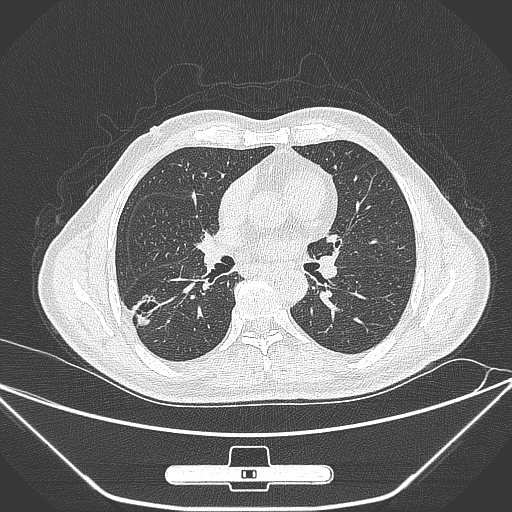
Chest CT, one axial slice; 120 kVp; lung window (W 1500 / L -600 HU); 512 × 512 image matrix, field of view 398 × 398 mm. Patient: male, 71 years. From the clinical record (not read from this slice): clinical TNM (as recorded): T1c N0 M0; histopathological grade: G2.
Outlined on this slice (bounding box drawn by a radiologist):
- lung tumour (recorded histology: adenocarcinoma): box from (x=125, y=287) to (x=166, y=333) px